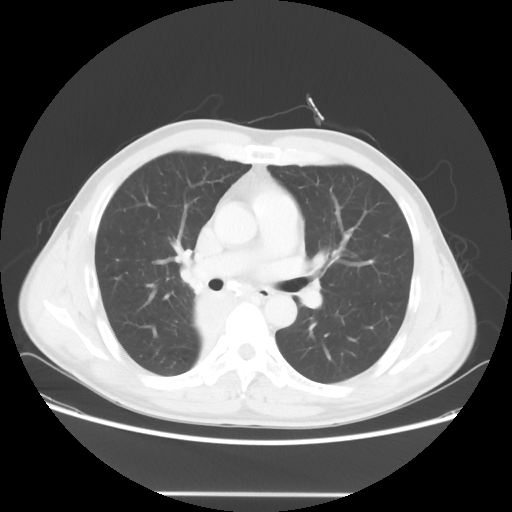
Chest CT, one axial slice; position 36 of 62 along the scan axis; lung window (W 1500 / L -600 HU); 5 mm slice thickness; 512 × 512 image matrix, field of view 393 × 393 mm. Male patient, age 47 years. Case-level facts recorded for this patient, not image findings: clinical TNM (as recorded): T2 N0 M0.
Annotated regions visible in this slice (rectangle marked by the reading radiologist):
- lung tumour (recorded histology: squamous cell carcinoma): box from (x=184, y=283) to (x=241, y=354) px